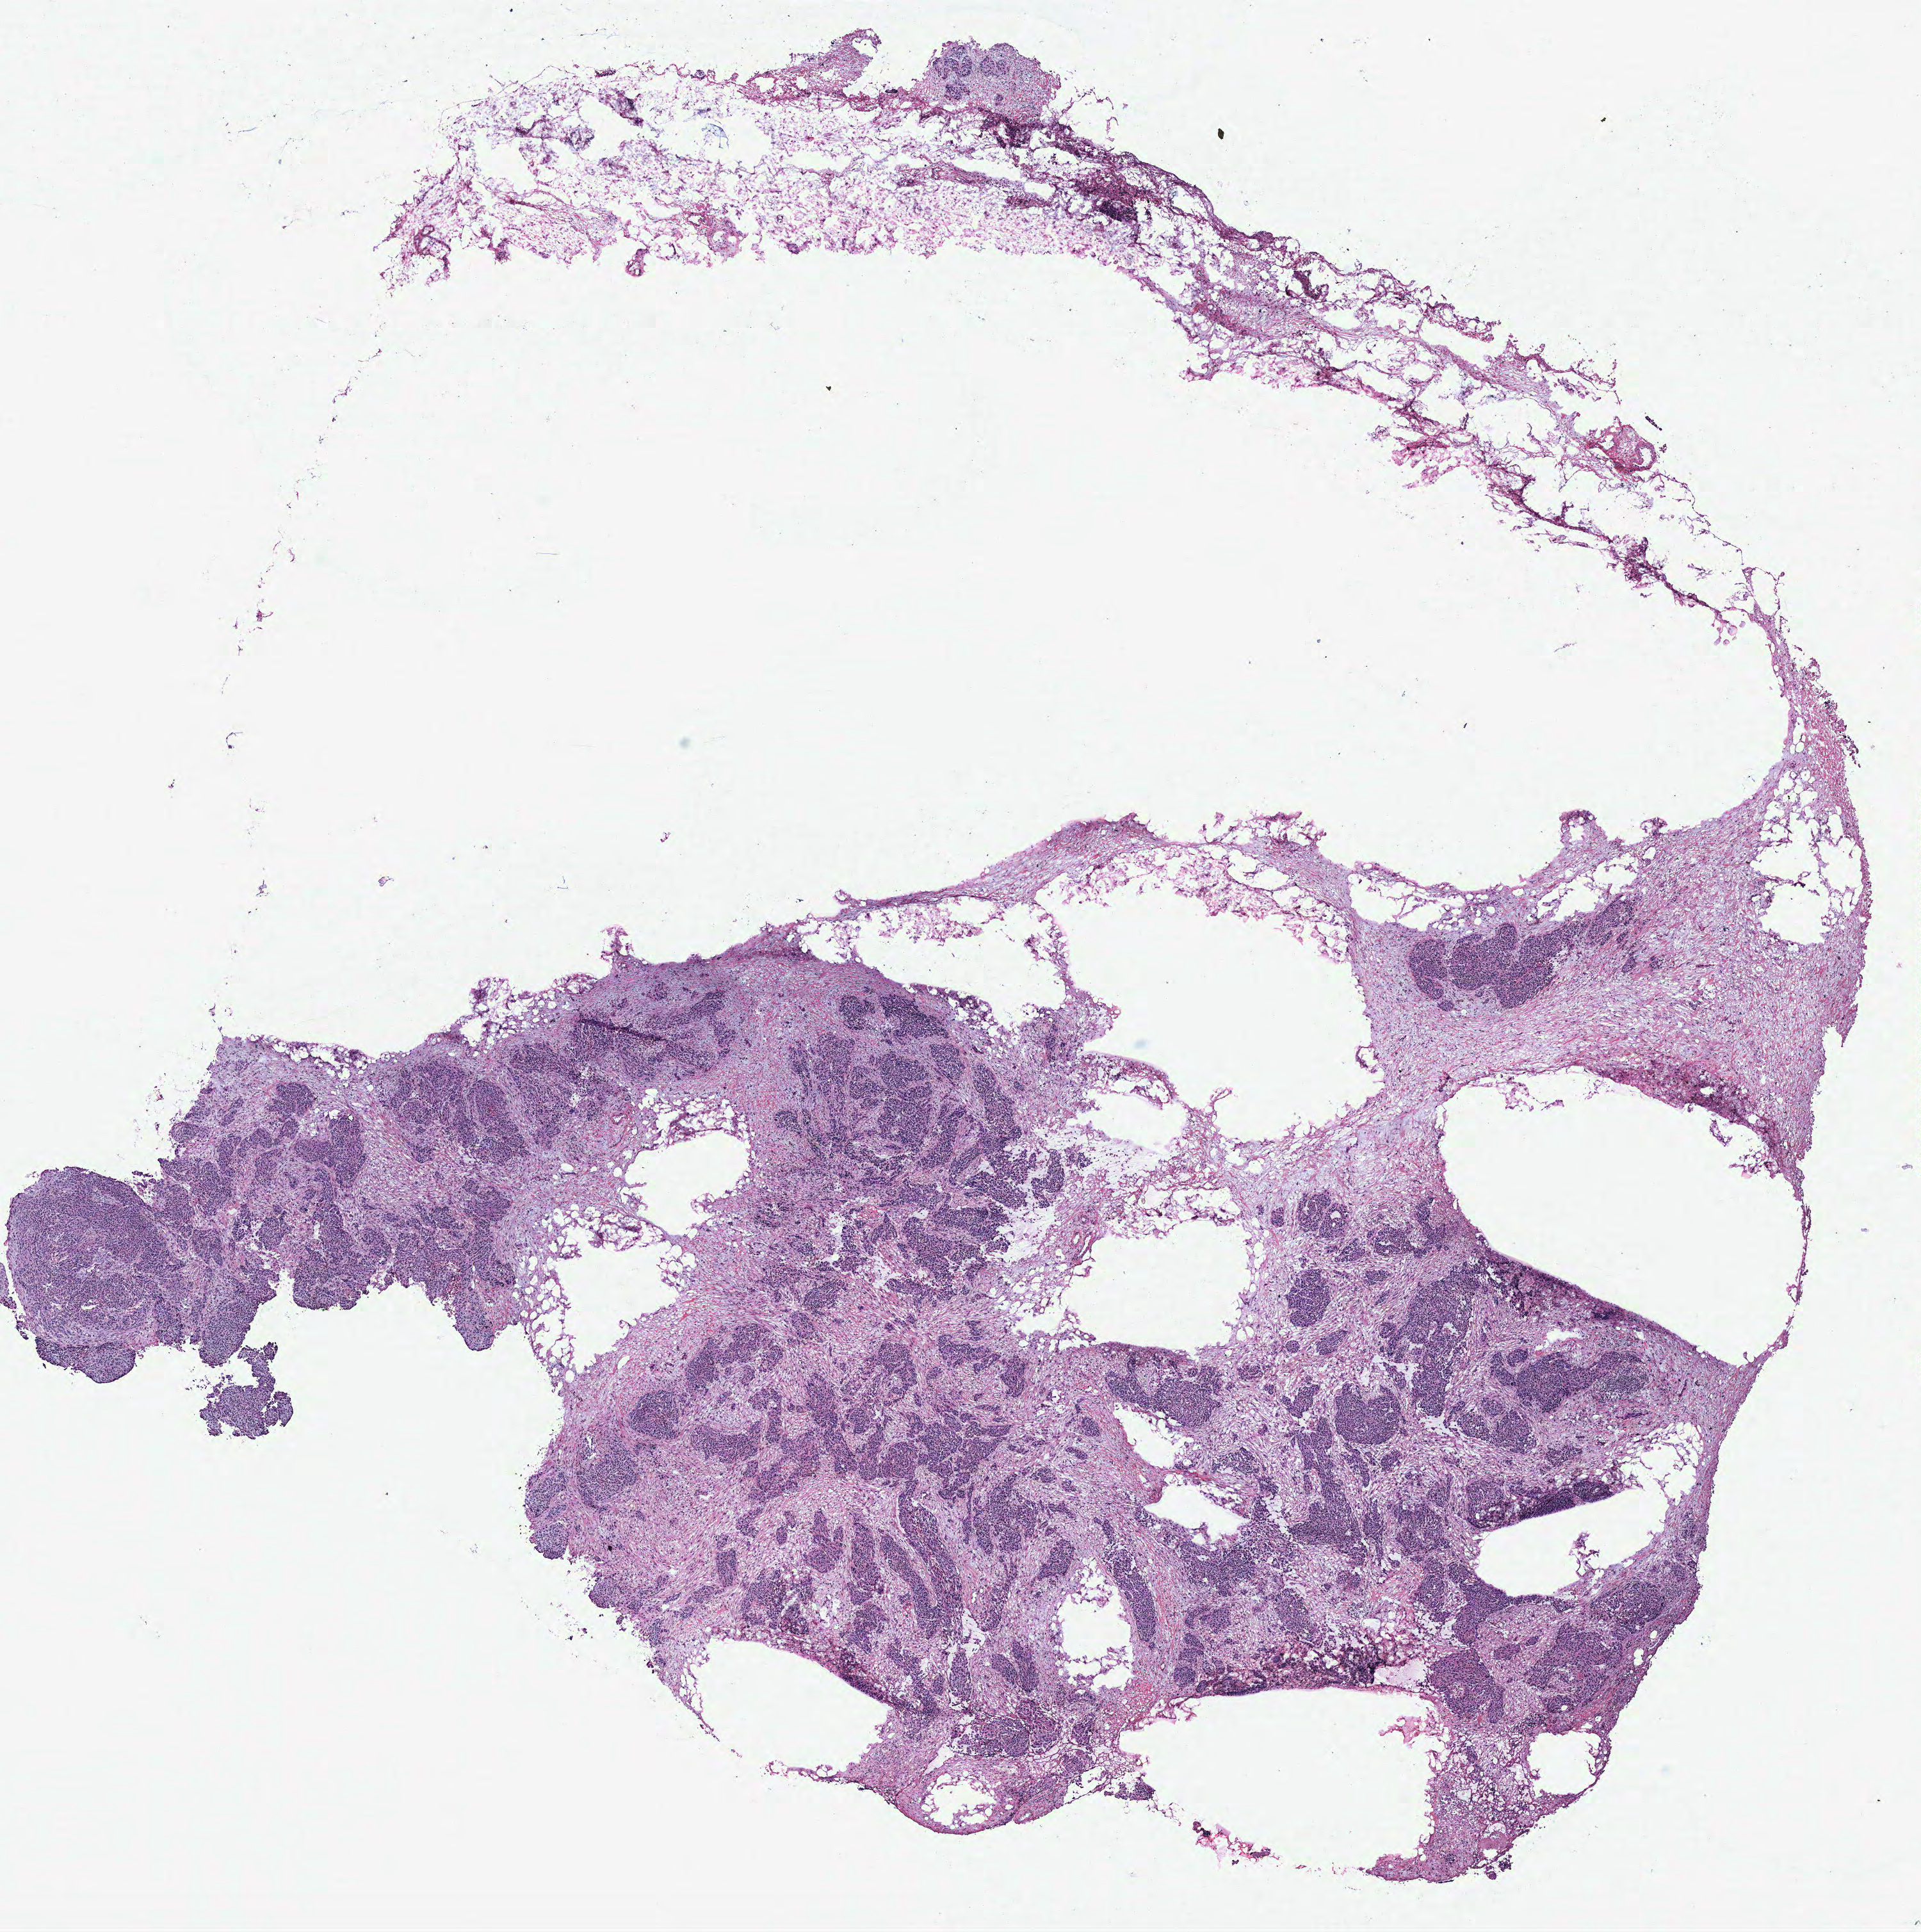
H&E whole-slide image, a low-resolution overview of the entire scanned area, about 12.0 x 12.1 mm (from a 40x scan); tumour tissue sample, ovary. 63-year-old female patient.
Diagnosis: Serous adenocarcinoma, NOS. Primary tumour site (as recorded): fallopian tube.